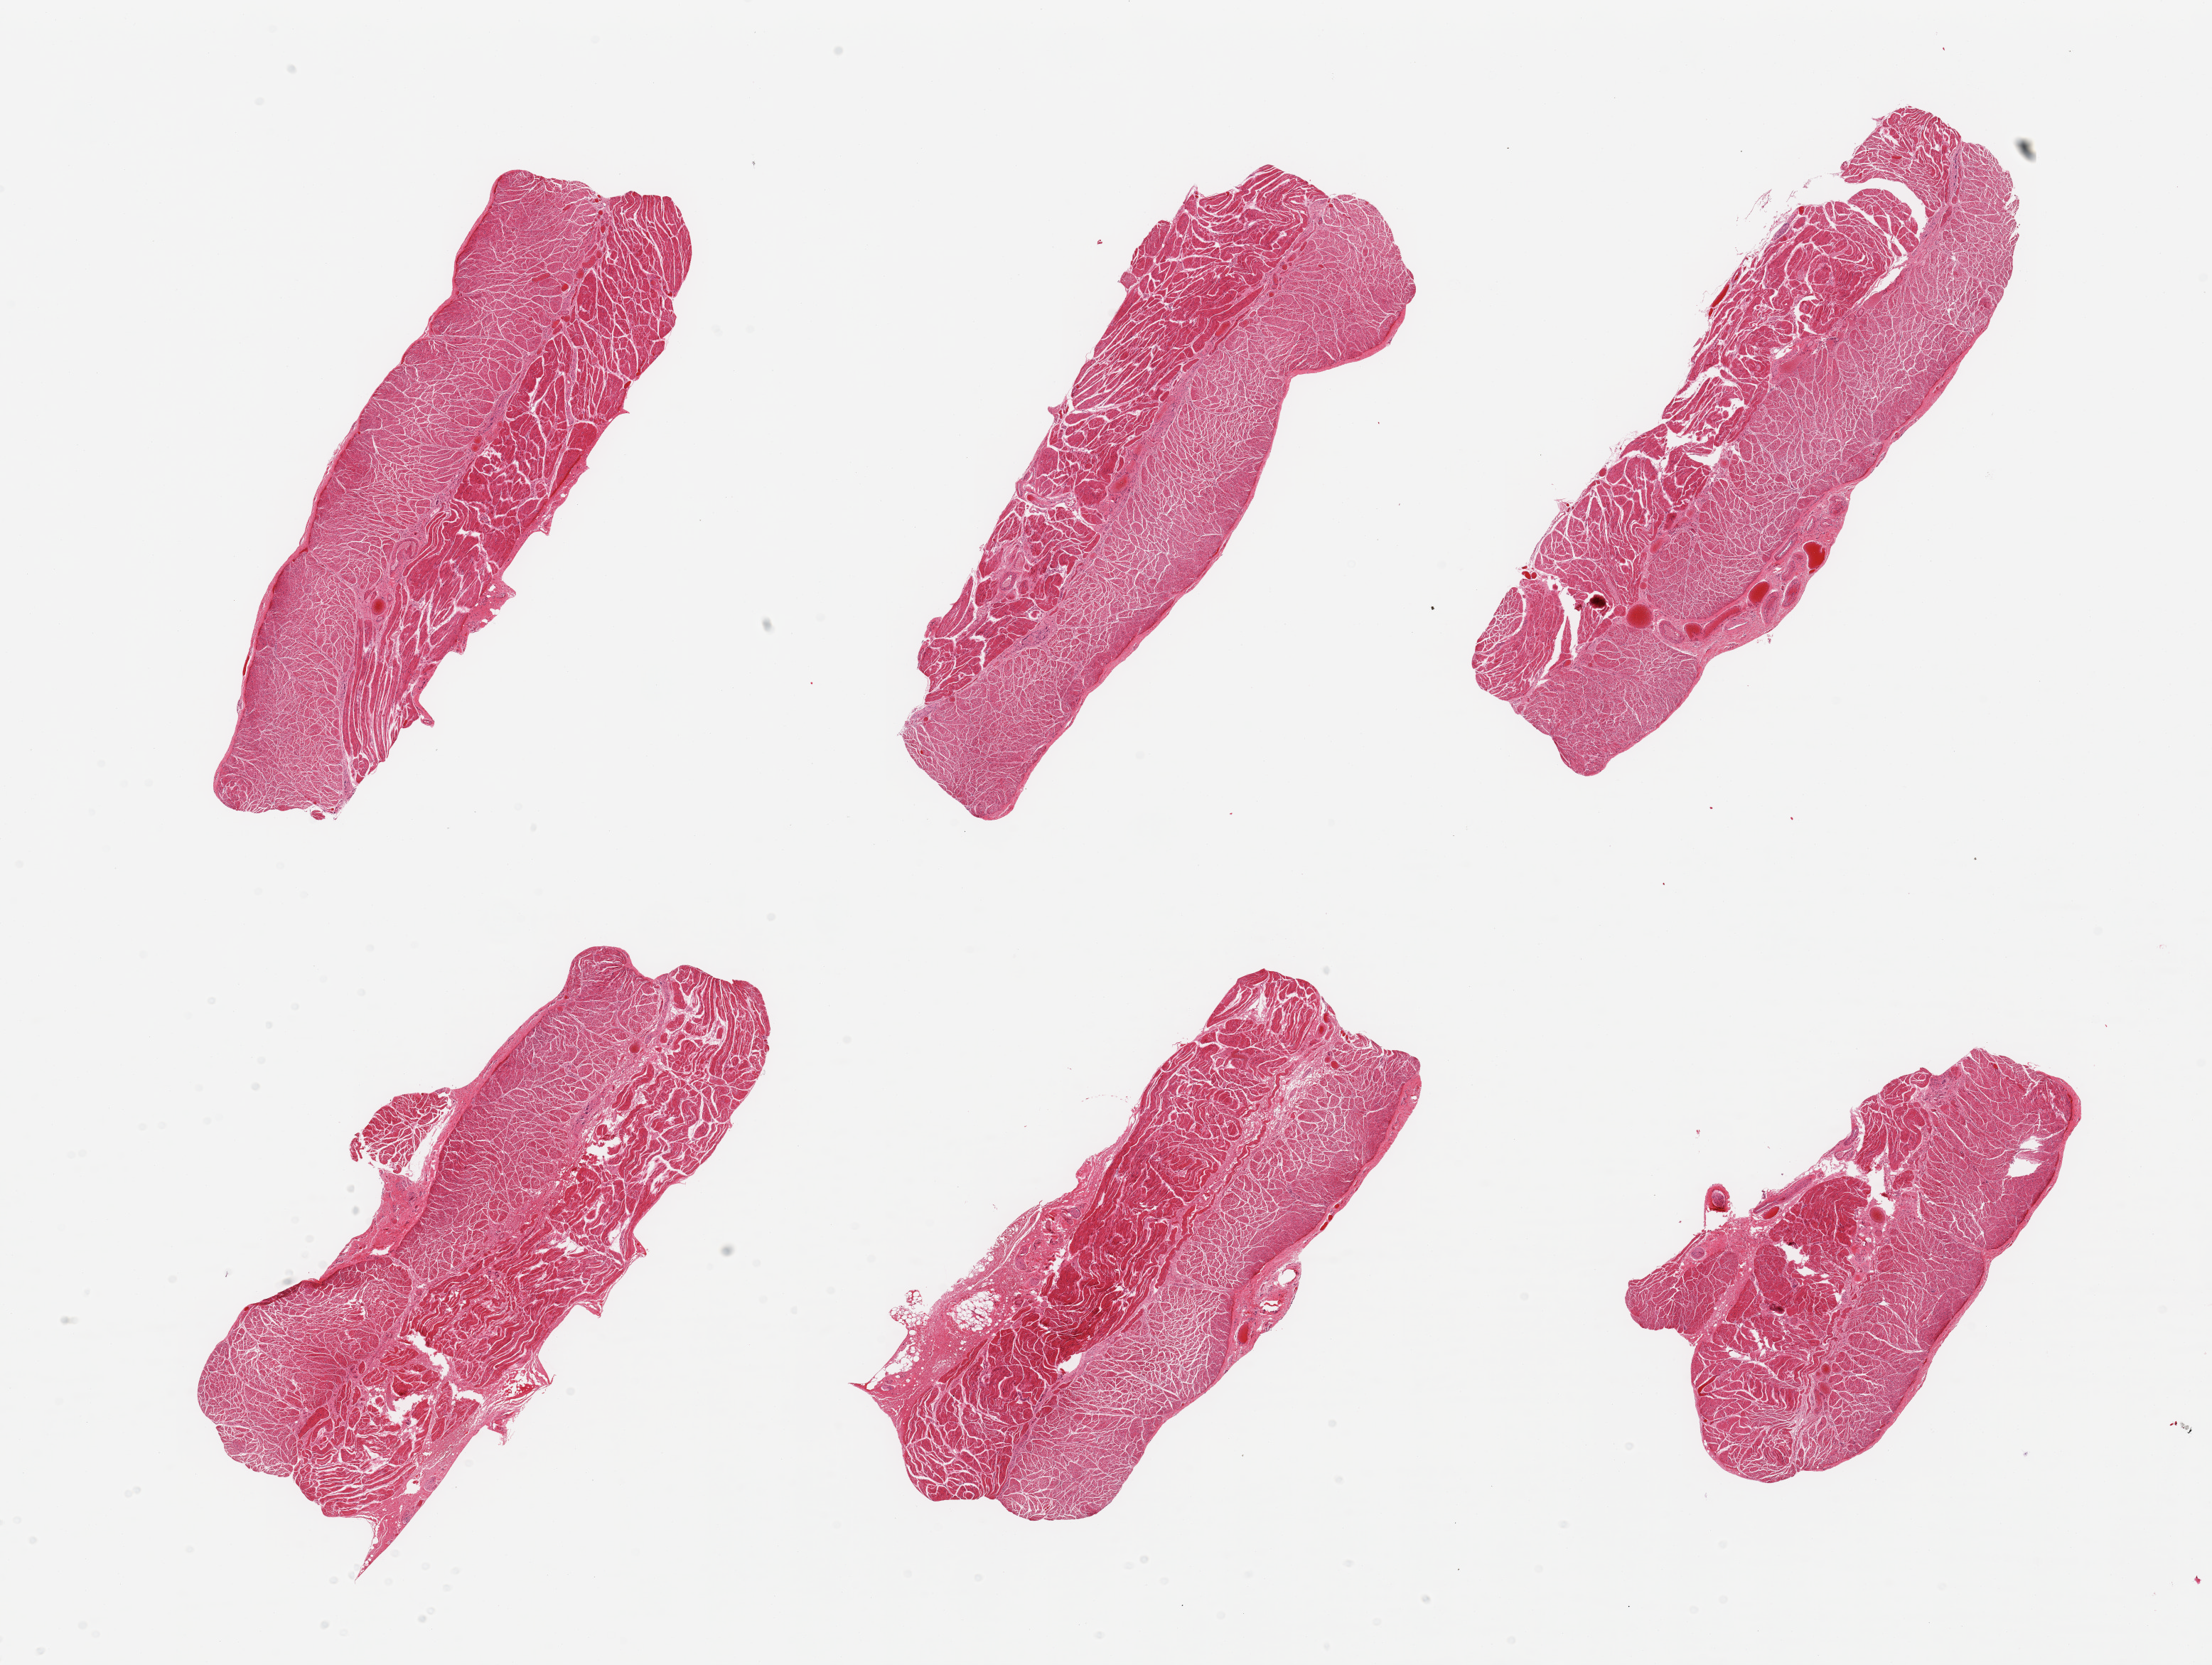
Whole-slide image, haematoxylin and eosin stain, shown as a low-resolution overview of the whole scanned area (about 24.6 x 18.5 mm), PAXgene-fixed, paraffin-embedded tissue, sampled site (target tissue): esophageal muscle, donor tissue sample. Donor sex: male.
Pathologist's review note for this sample: 6 pieces; well dissected muscularis.